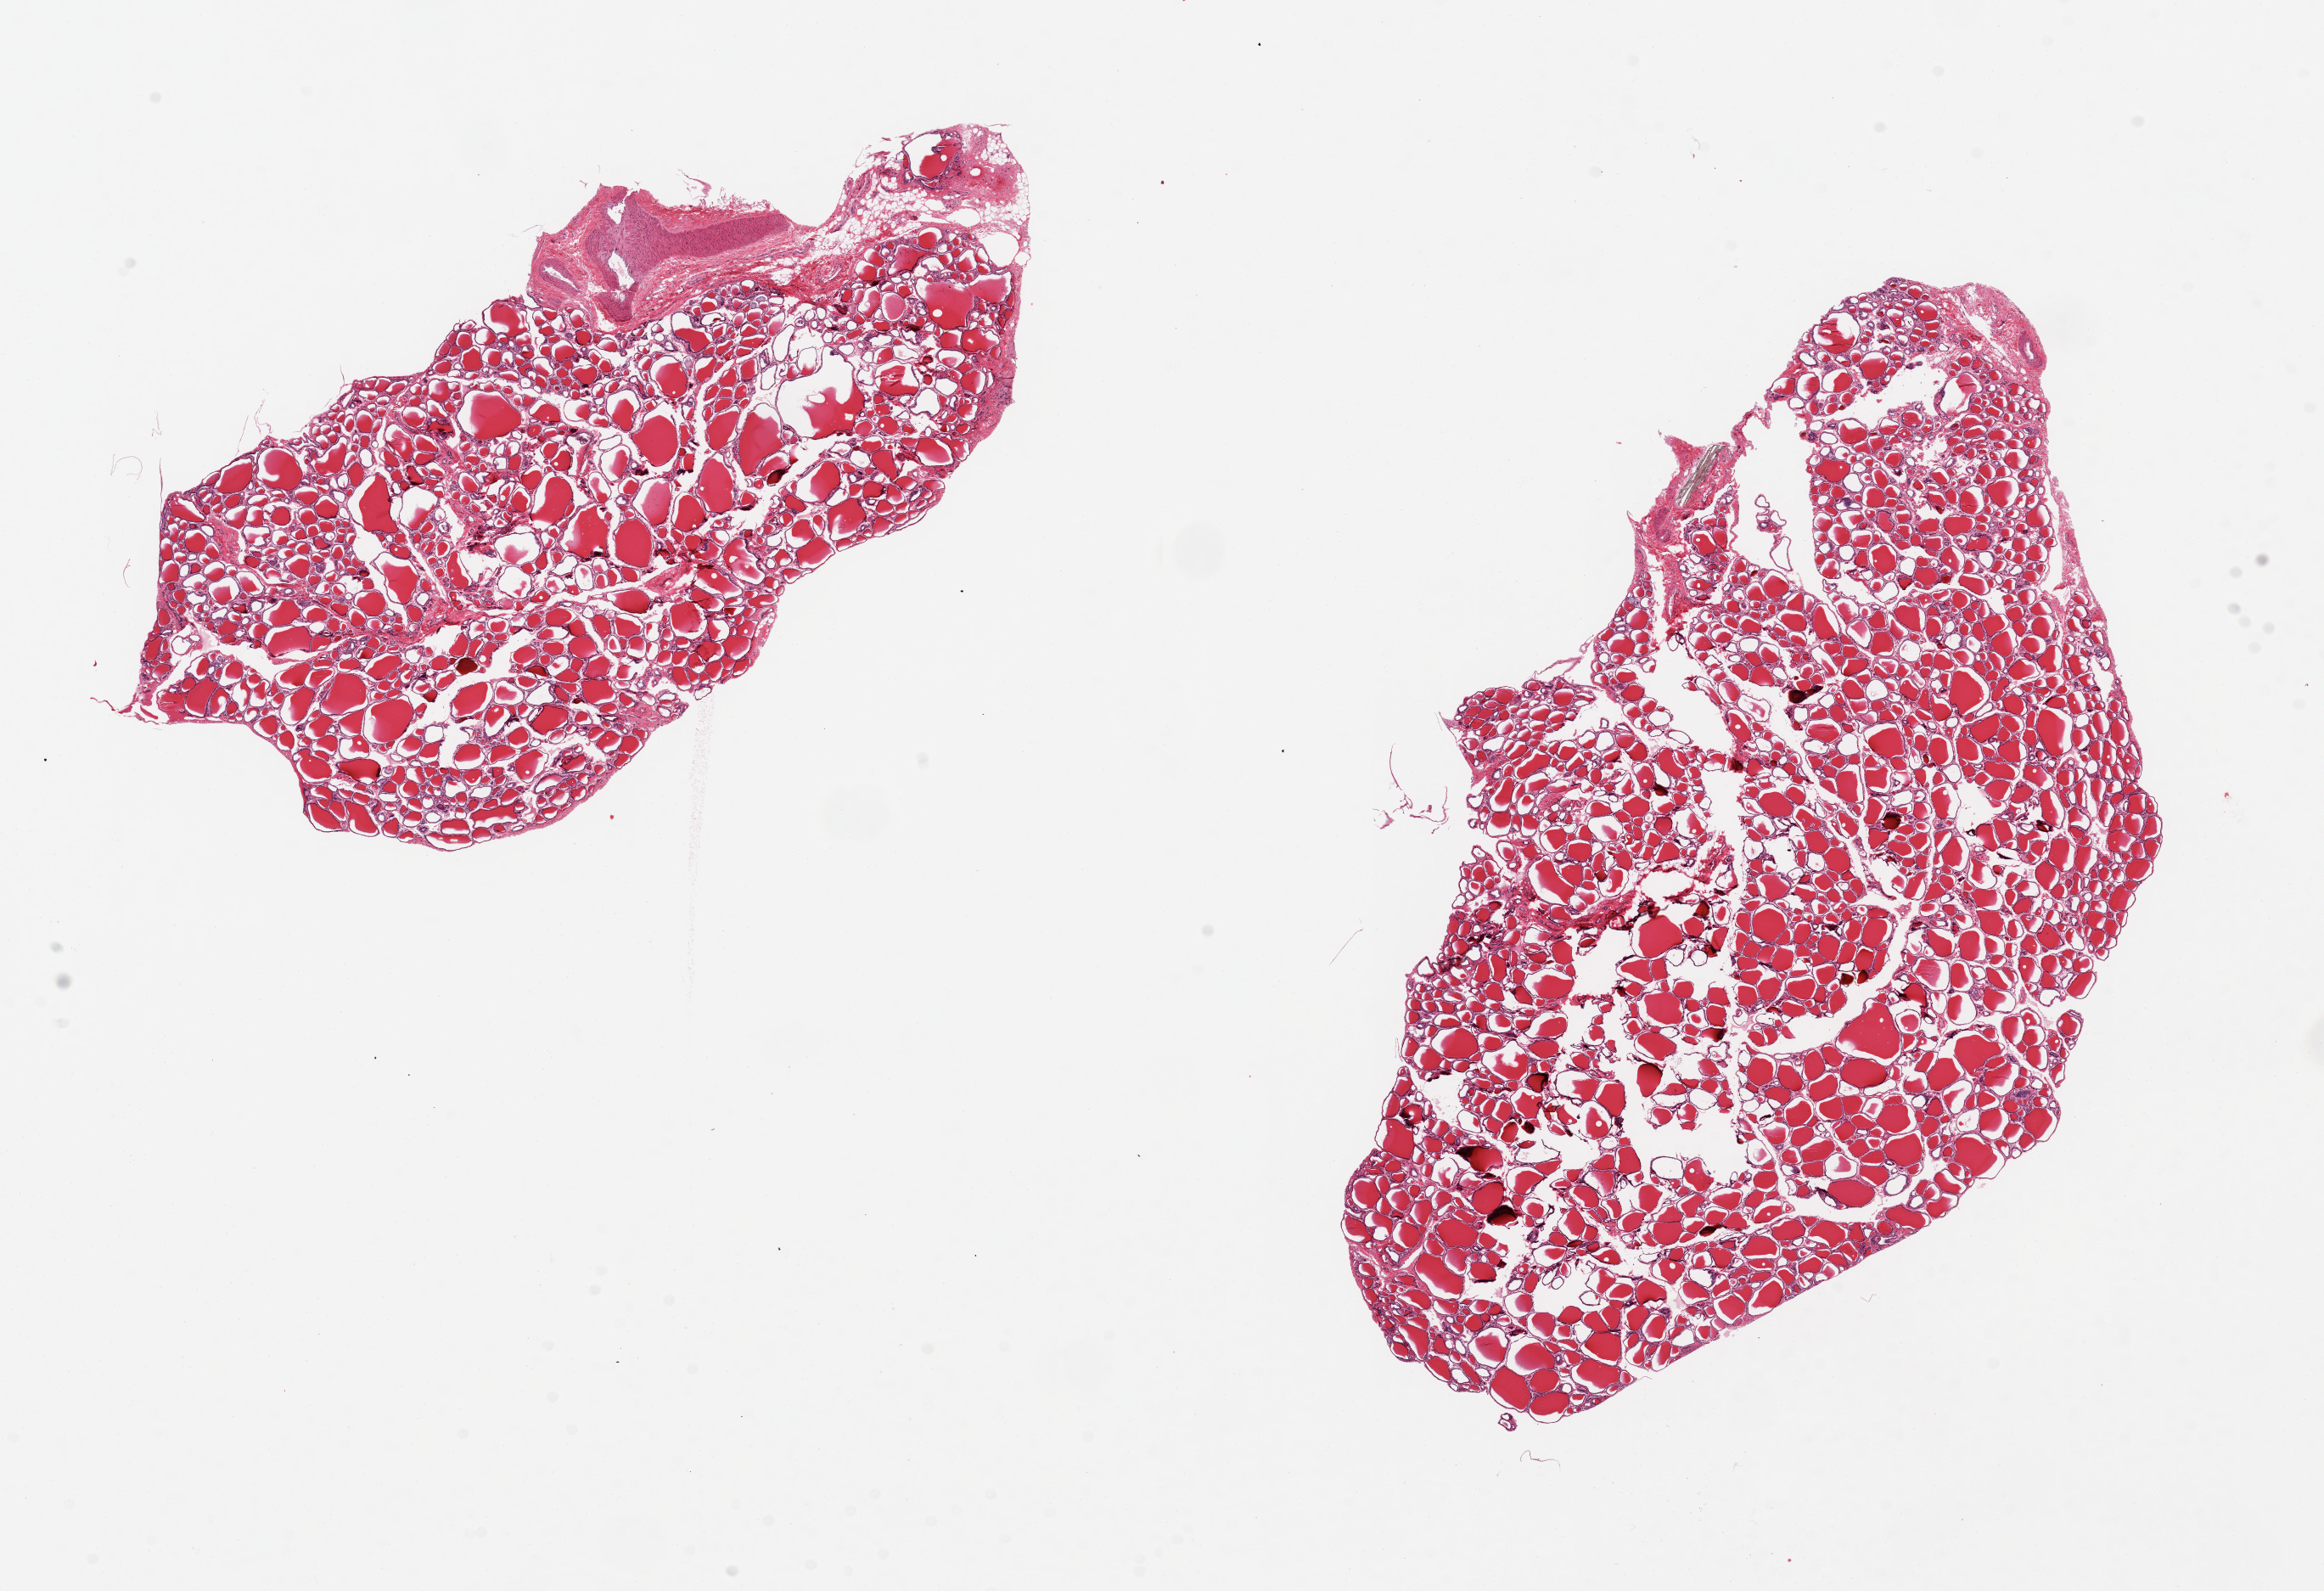
Whole-slide image, haematoxylin and eosin stain, a low-resolution overview of the entire scanned area, about 21.7 x 14.8 mm (from a 20x scan). PAXgene-fixed, paraffin-embedded tissue. Sampled site (target tissue): thyroid. Donor tissue sample. Donor sex: male.
Reviewer comment on this tissue sample: 2 pieces 11x6 & 9x4 mm; focus of blood vessels at edge of one aliquot.